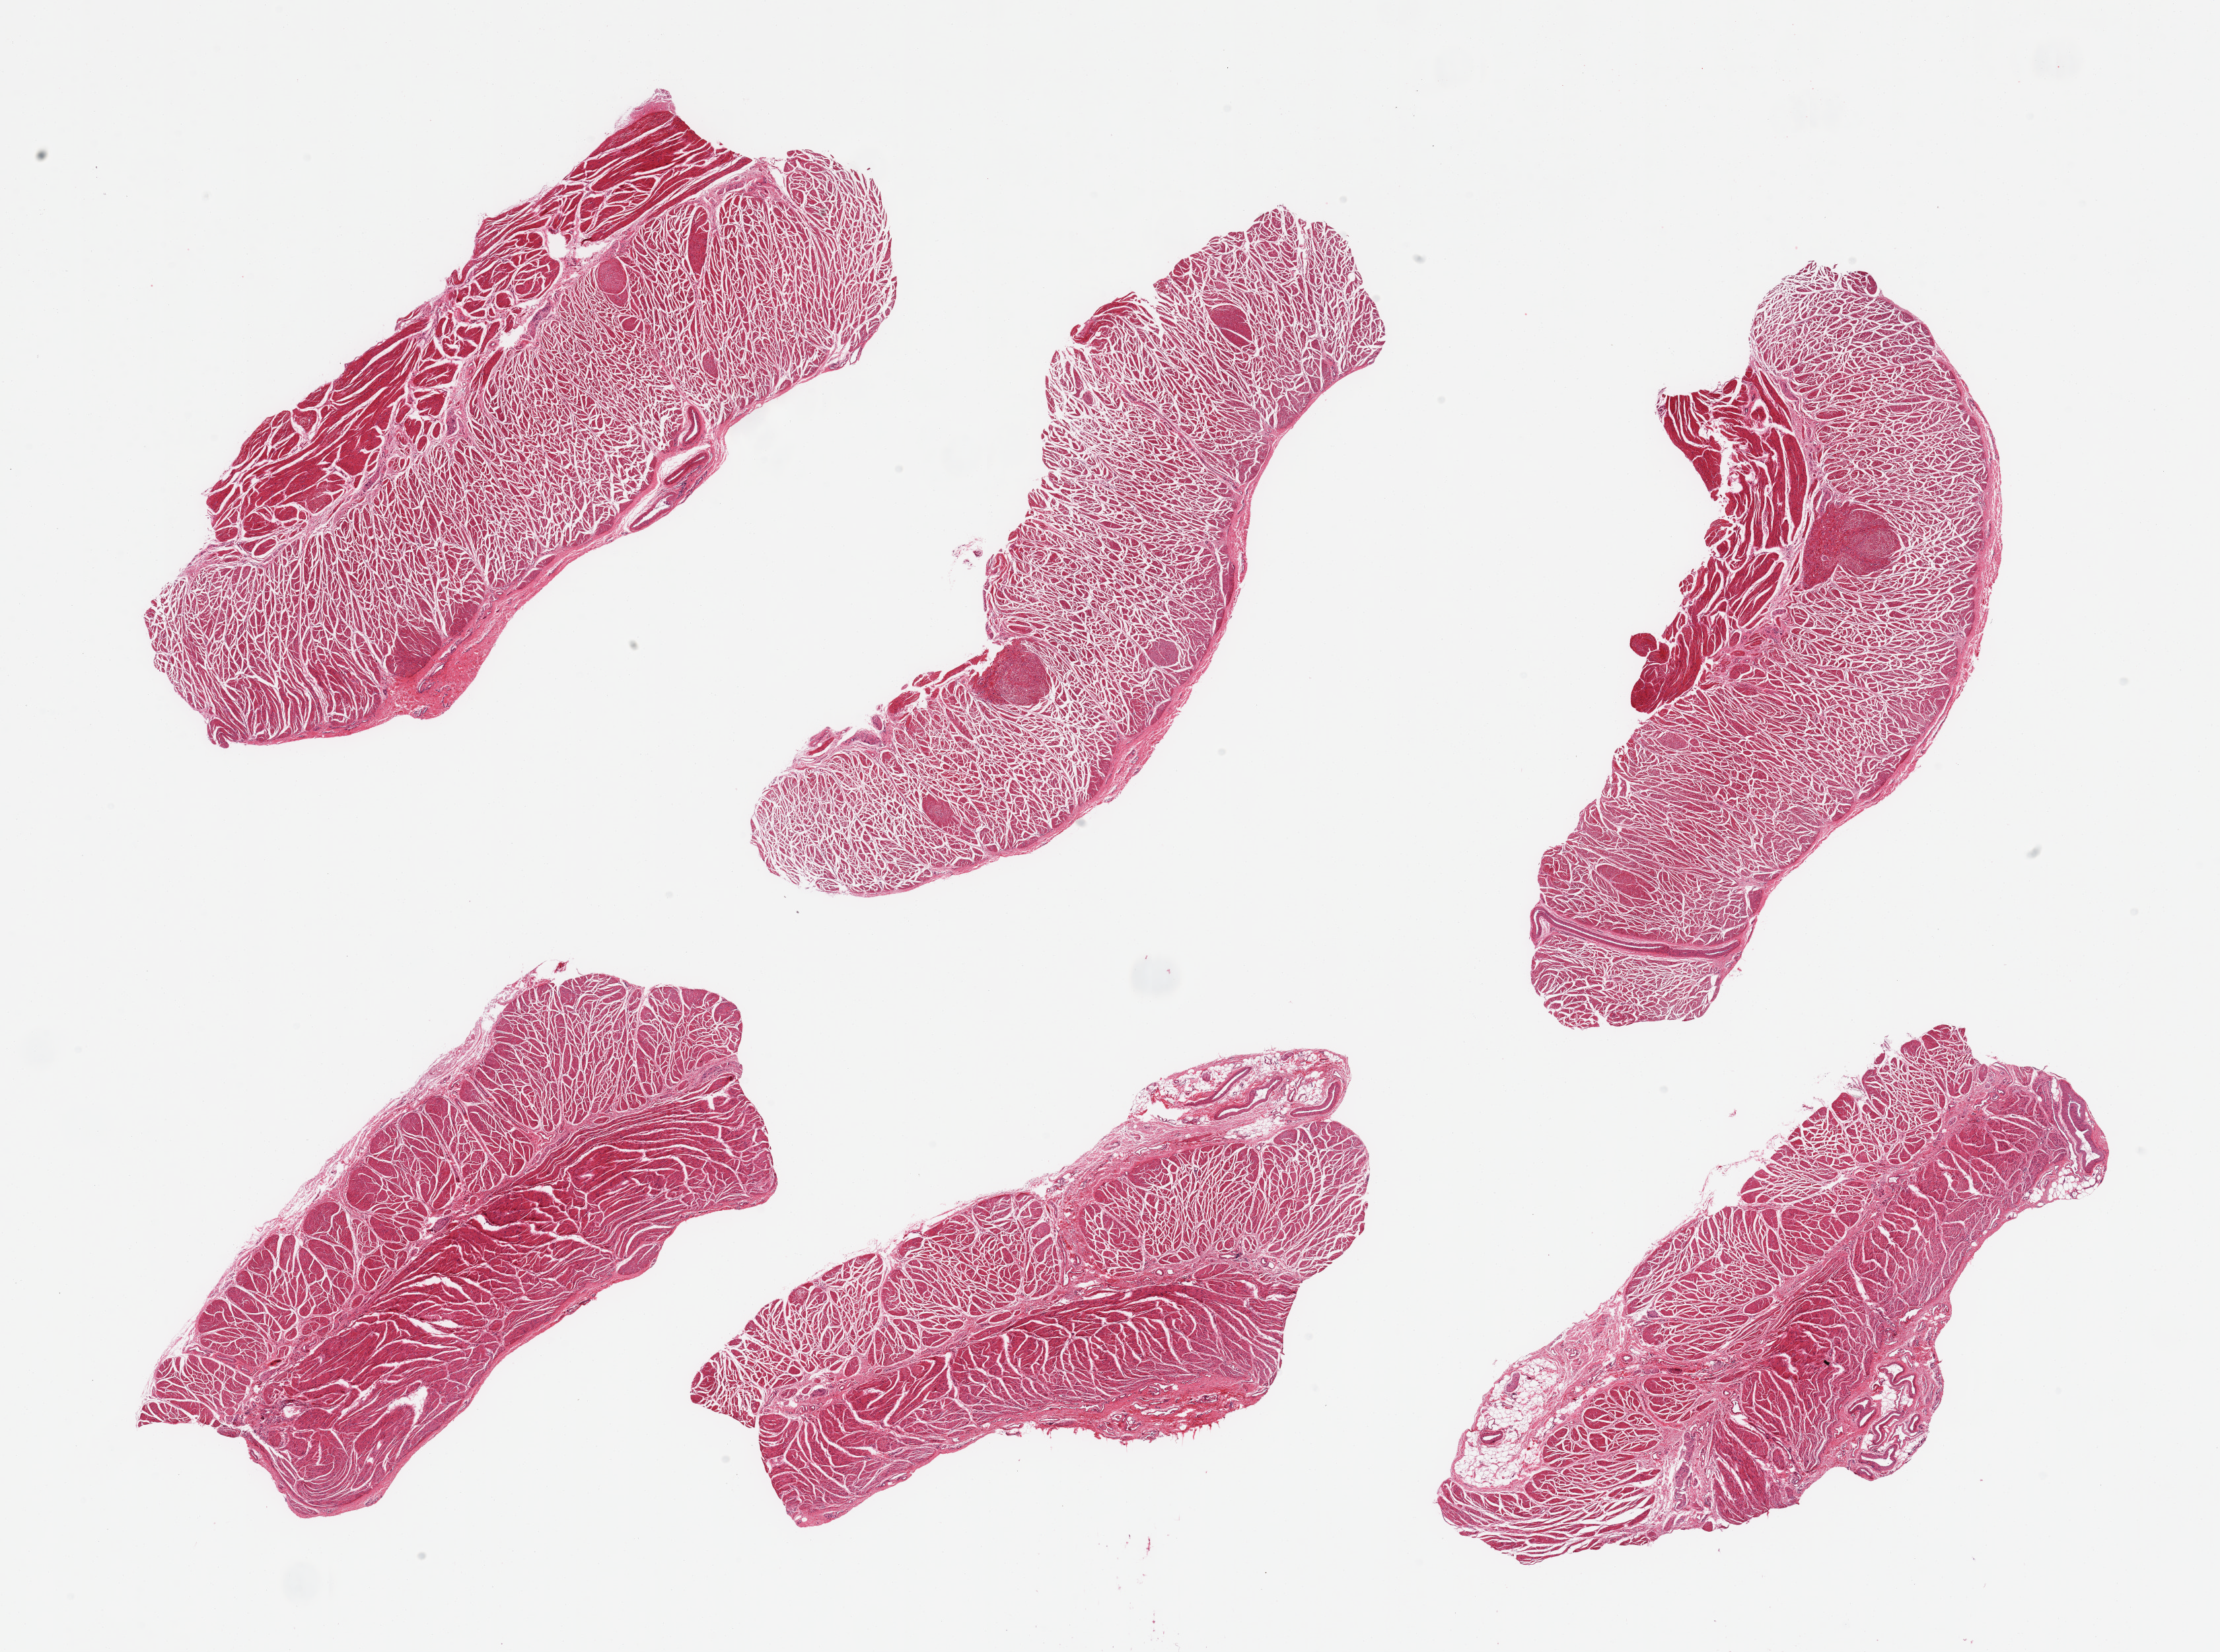
H&E whole-slide image, a low-resolution overview of the entire scanned area, about 26.6 x 19.8 mm, PAXgene-fixed, paraffin-embedded tissue, target tissue: gastroesophageal junction, tissue donor sample. Male donor.
• pathologist's review note for this sample: 6 pieces; multiple seedling leiomyomas (<1 mm) in 3 of 6 pieces